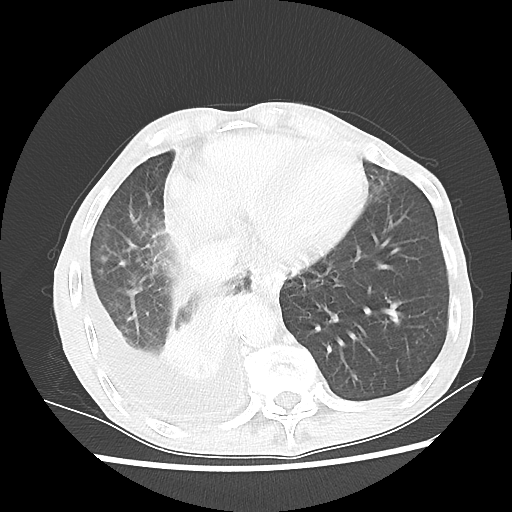
Chest CT, one axial slice; position 17 of 60 along the scan axis; reconstruction kernel LUNG; 80 kVp; lung window (W 1500 / L -600 HU); 5 mm slice thickness; 512 × 512 image matrix. Male patient, age 76 years. From the clinical record (not read from this slice): clinical TNM (as recorded): T3 N3 M1a.
Annotated regions visible in this slice (rectangle marked by the reading radiologist):
- lung tumour (recorded histology: squamous cell carcinoma): box from (x=154, y=294) to (x=241, y=380) px